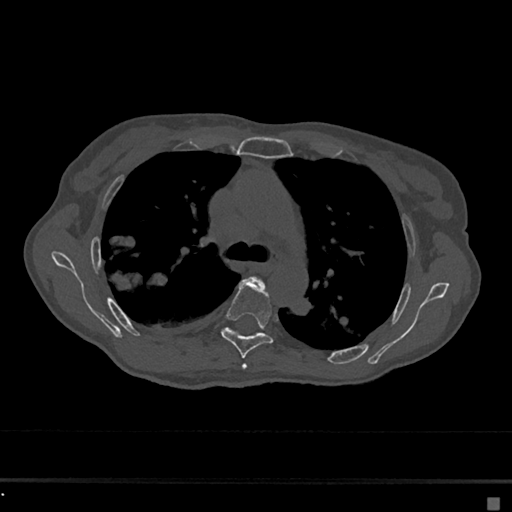
CT including the spine, one axial slice; slice 461 of 797 in the series (ordered by position); reconstruction kernel Br40s/3; bone window (W 1800 / L 400 HU); 0.5 mm slice thickness; 512 × 512 image matrix, field of view 360 × 360 mm. Patient: female, 68 years. From the clinical record (not read from this slice): primary cancer: renal.
Outlined on this slice (semi-automatic segmentation, software-assisted and operator-edited):
- T4 vertebra: box from (x=241, y=276) to (x=265, y=370) px
- T5 vertebra: (x=220, y=279)–(x=273, y=359)
- T6 vertebra: (x=227, y=328)–(x=234, y=332)